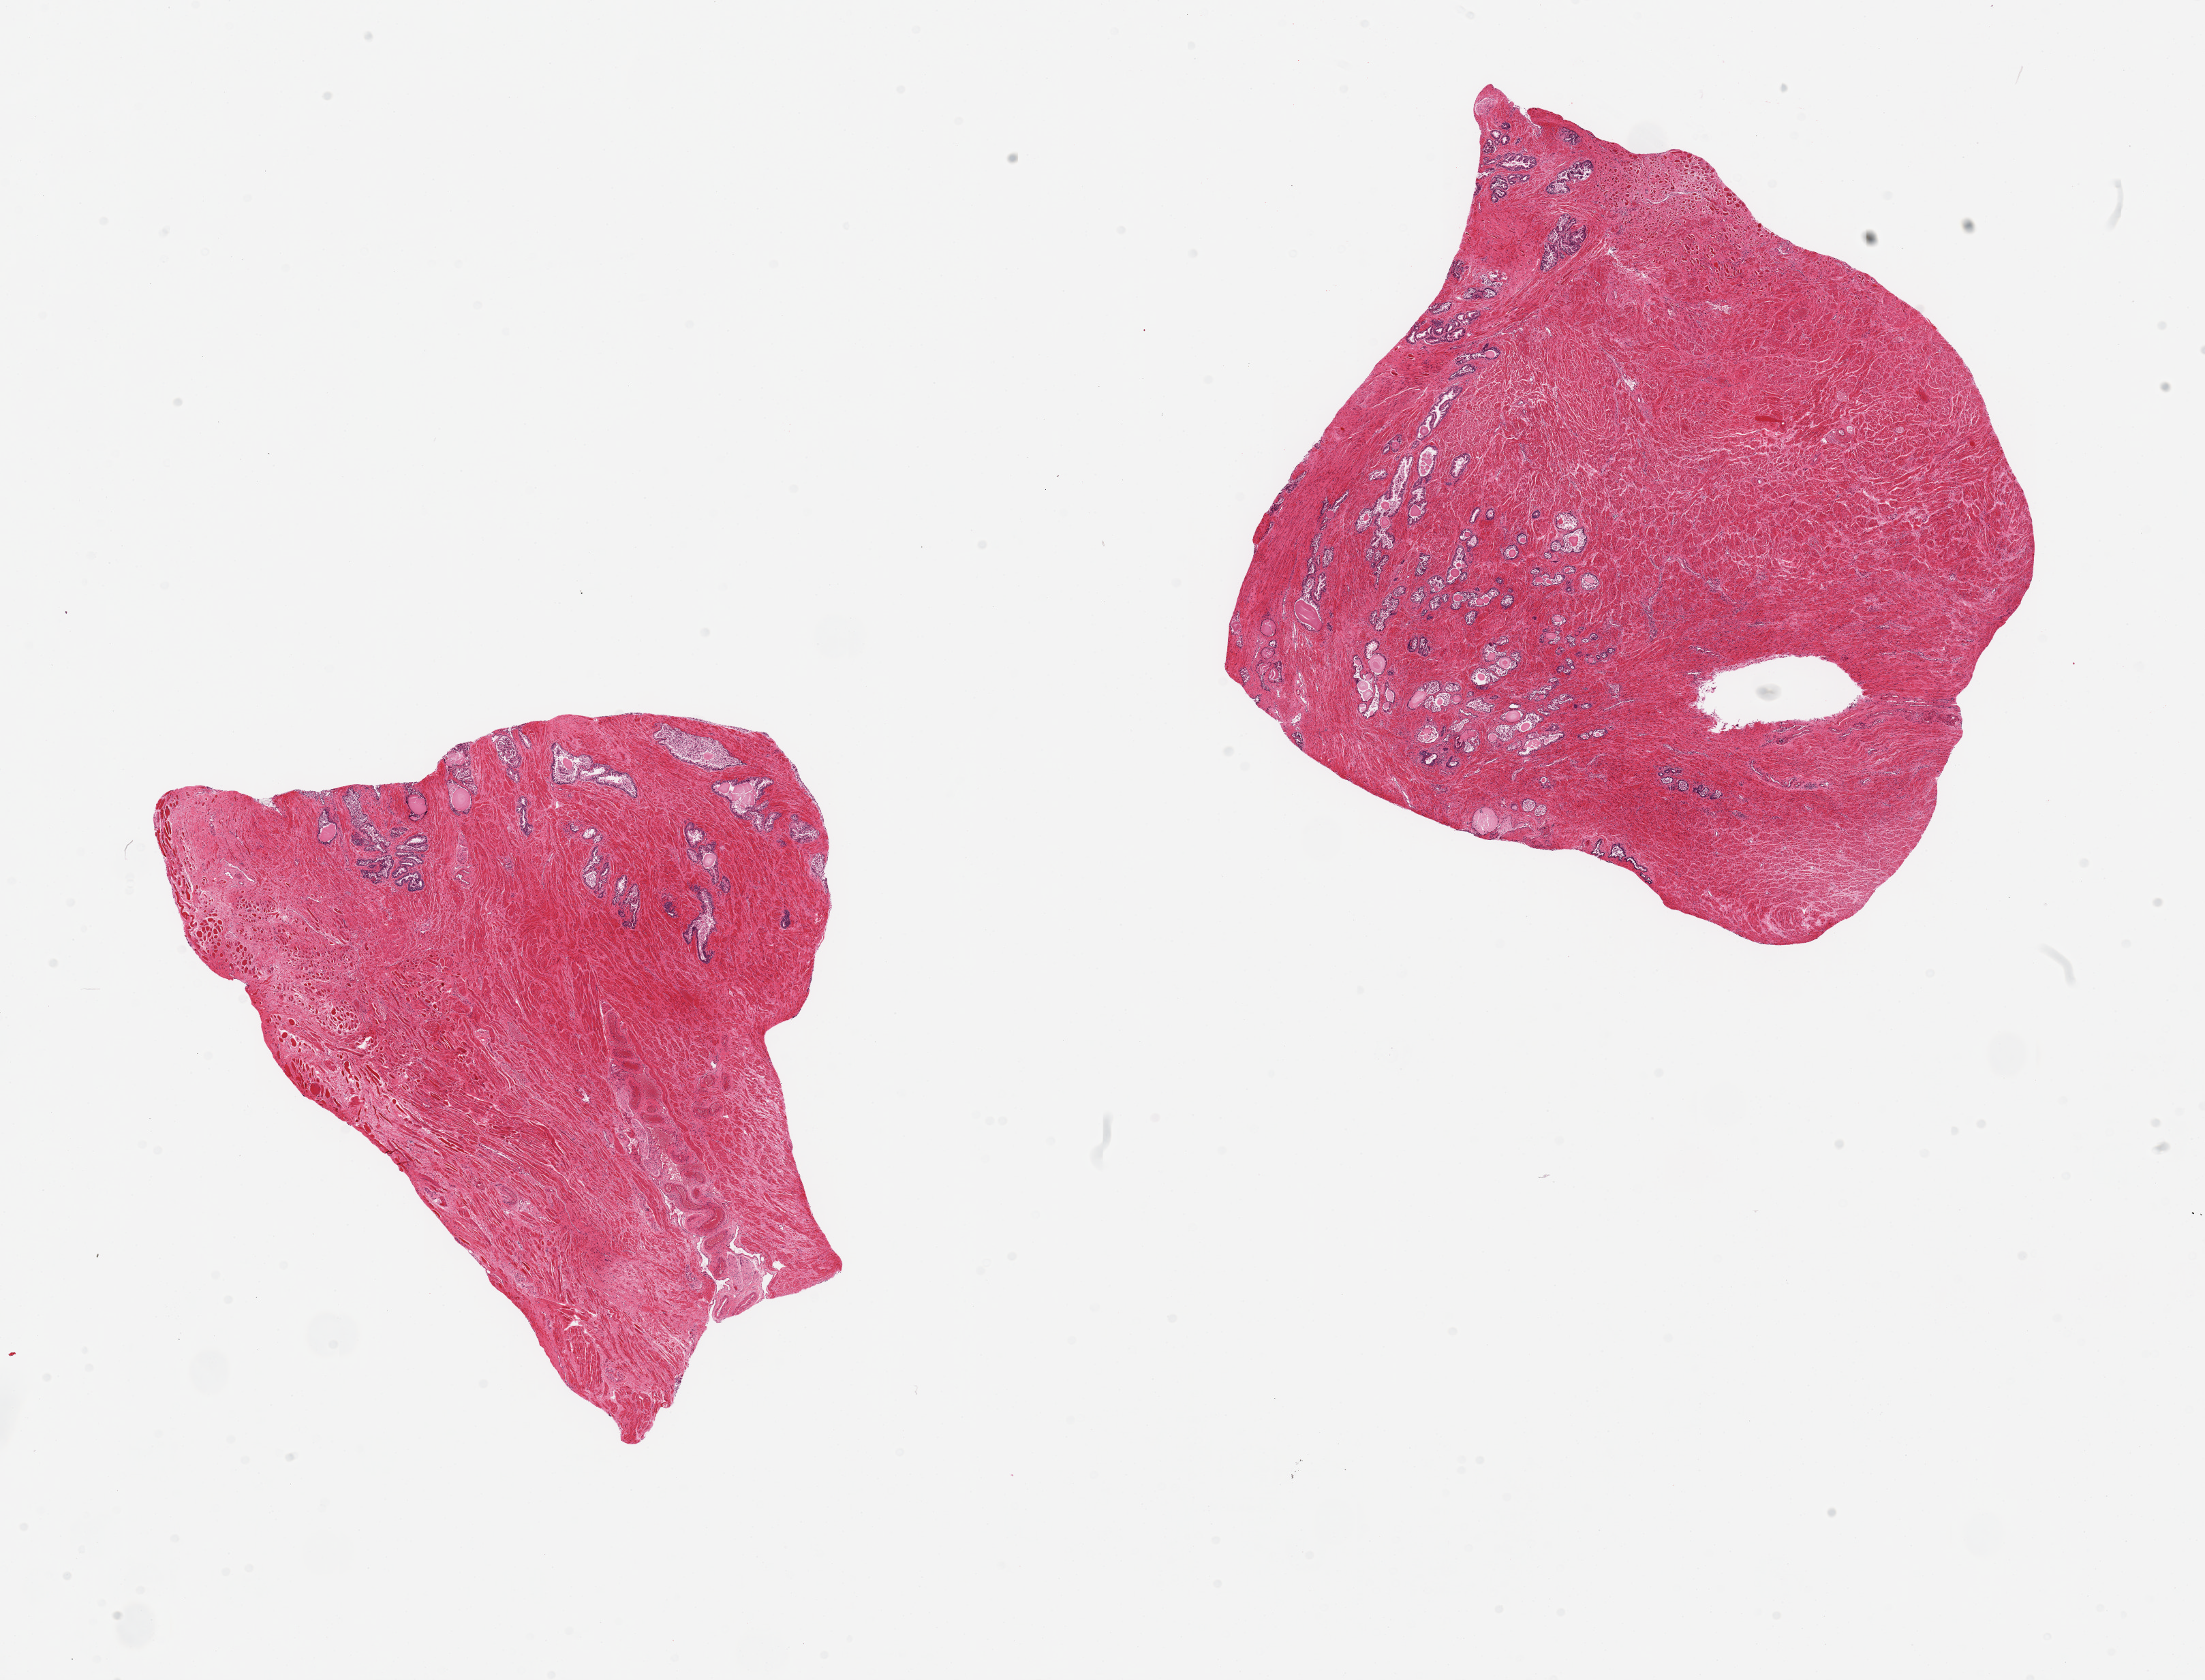
Digitized hematoxylin and eosin (H&E)-stained section, low-resolution overview of the scanned area, about 25.6 x 19.5 mm (from a 20x scan), PAXgene-fixed paraffin-embedded (PFPE) section, sampled site (target tissue): prostate, tissue donor sample. Male donor.
* pathologist's review note for this sample: 2 pieces, glandular elements moderately autolyzed, partially sloughing